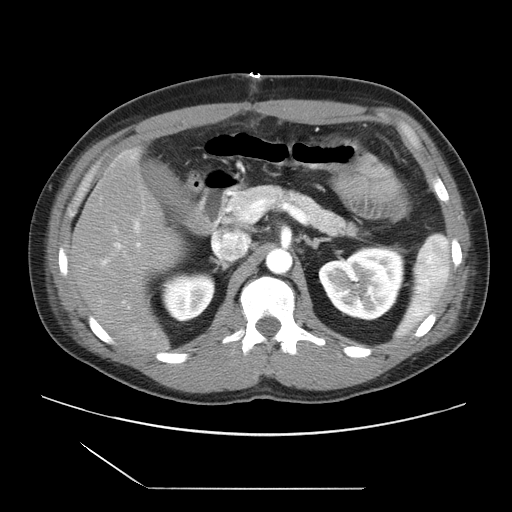
Contrast-enhanced abdominal CT, one axial slice; slice 12 of 39 in the series (ordered by position); intravenous contrast given; soft-tissue window (W 400 / L 40 HU); 5 mm slice thickness; 512 × 512 image matrix, field of view 395 × 395 mm. Male patient, age 39 years. Case-level facts recorded for this patient, not image findings: diagnosis: colorectal cancer liver metastases, imaged before liver resection; multiple liver metastases: yes; largest metastasis: 1.3 cm; disease in both lobes: no.
Annotated regions visible in this slice (expert manual segmentation):
- hepatic veins: box from (x=215, y=232) to (x=243, y=260) px
- liver: (x=68, y=151)–(x=182, y=355)
- portal vein (with intrahepatic branches): (x=101, y=209)–(x=239, y=304)